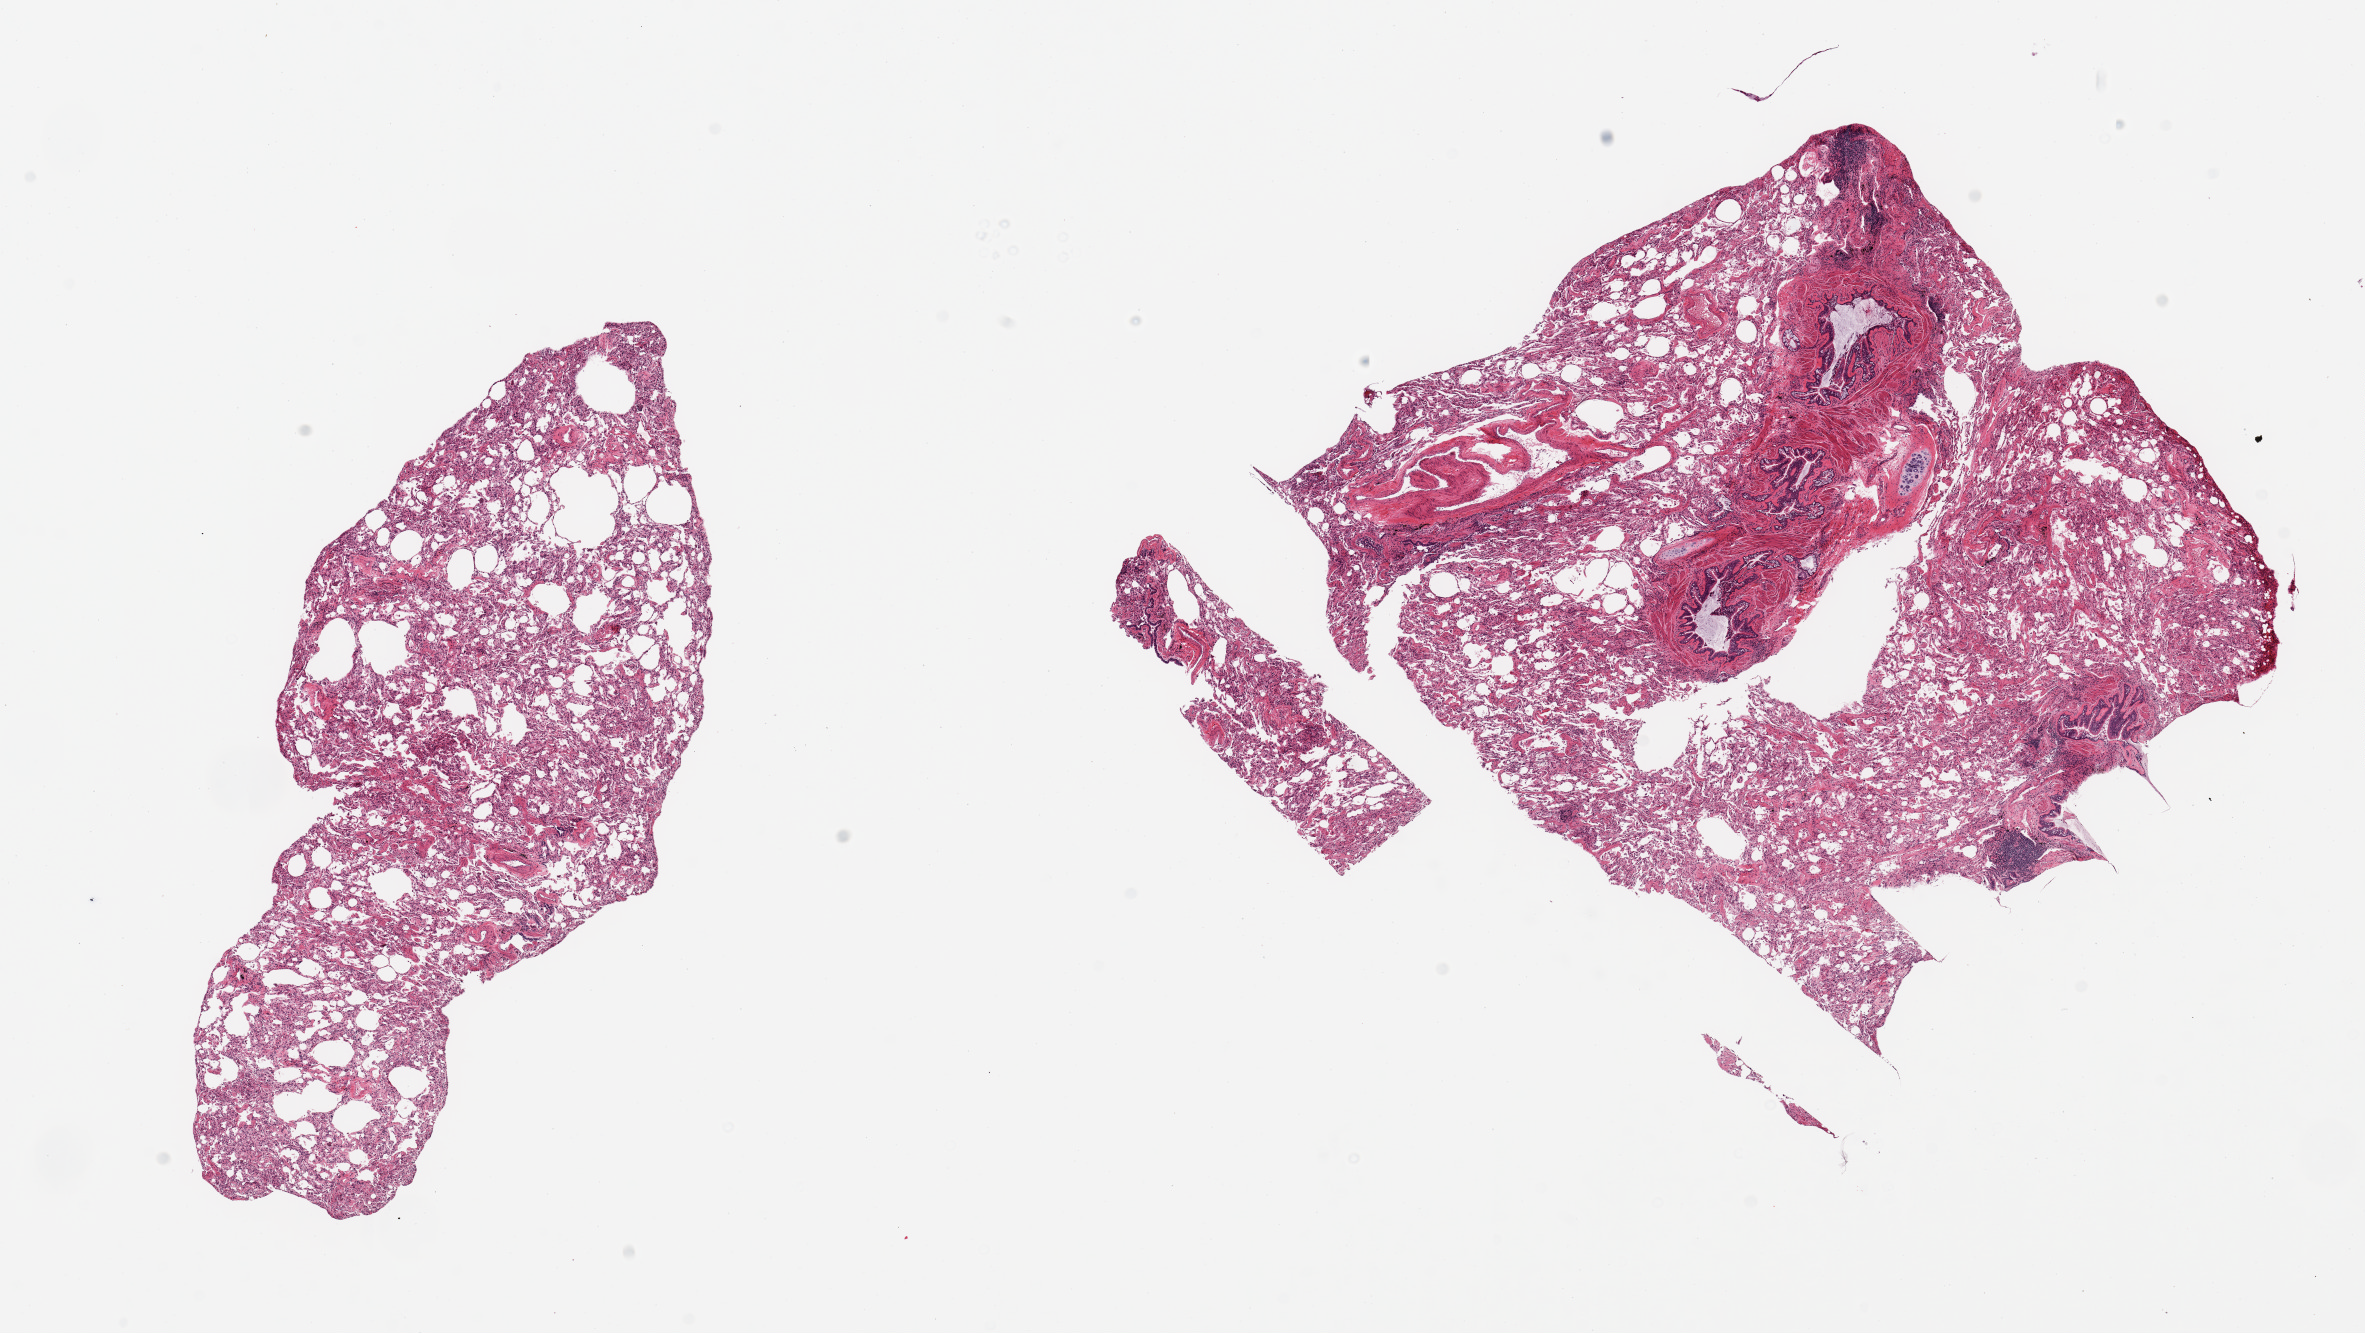
H&E whole-slide image, brightfield — low-resolution overview of the scanned area, about 18.7 x 10.5 mm. PAXgene-fixed, paraffin-embedded tissue. Target tissue: lung. Tissue donor sample. Female donor.
Review note (as recorded): 2 pieces; atelectasis alternating with dilated alveolar spaces; one piece contains bronchi with prominent smooth muscle, hyperplasia of submucosal mucous glands and peribronchial lymphocytic ifiltrate and cartlilage; thick-walled vessels; anthracosis.